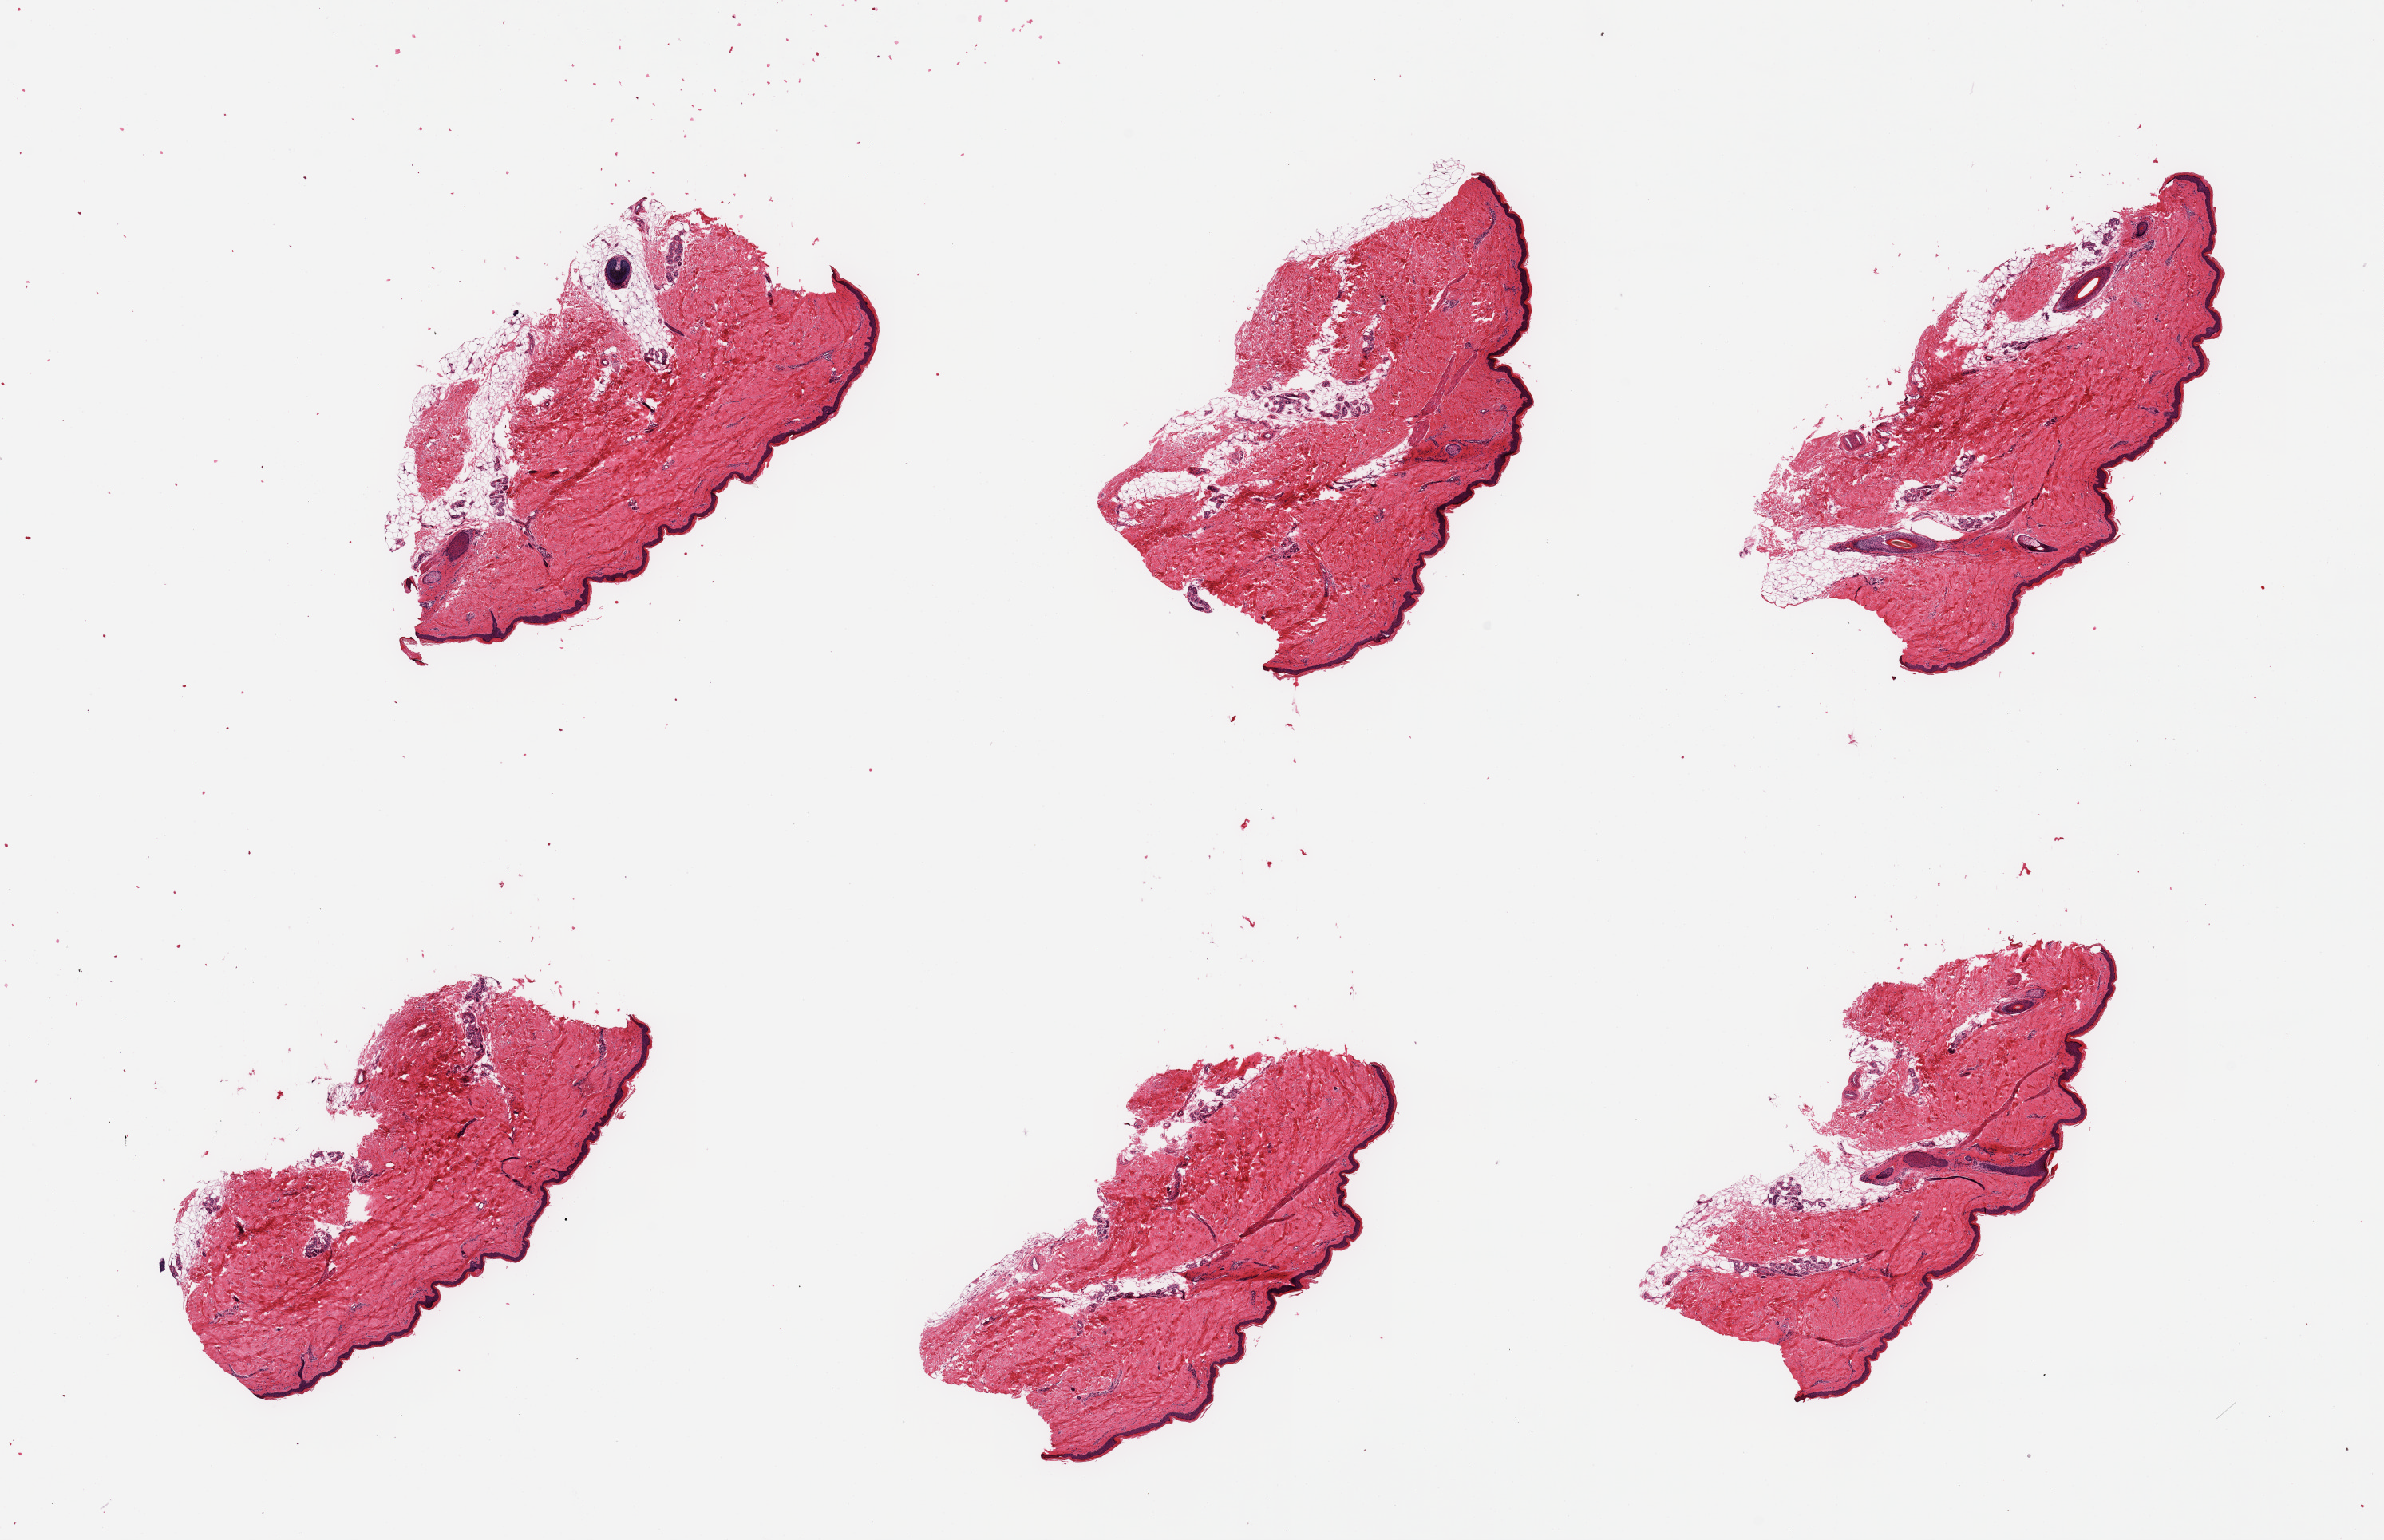
Digitized H&E-stained section, low-resolution overview of the scanned area, about 23.6 x 15.3 mm; PAXgene-fixed paraffin-embedded (PFPE) section; section of skin of lower leg (target tissue); tissue donor sample. Donor: female.
• reviewer comment on this tissue sample: 6 pieces; well trimmed with 5 - 20% dermal fat